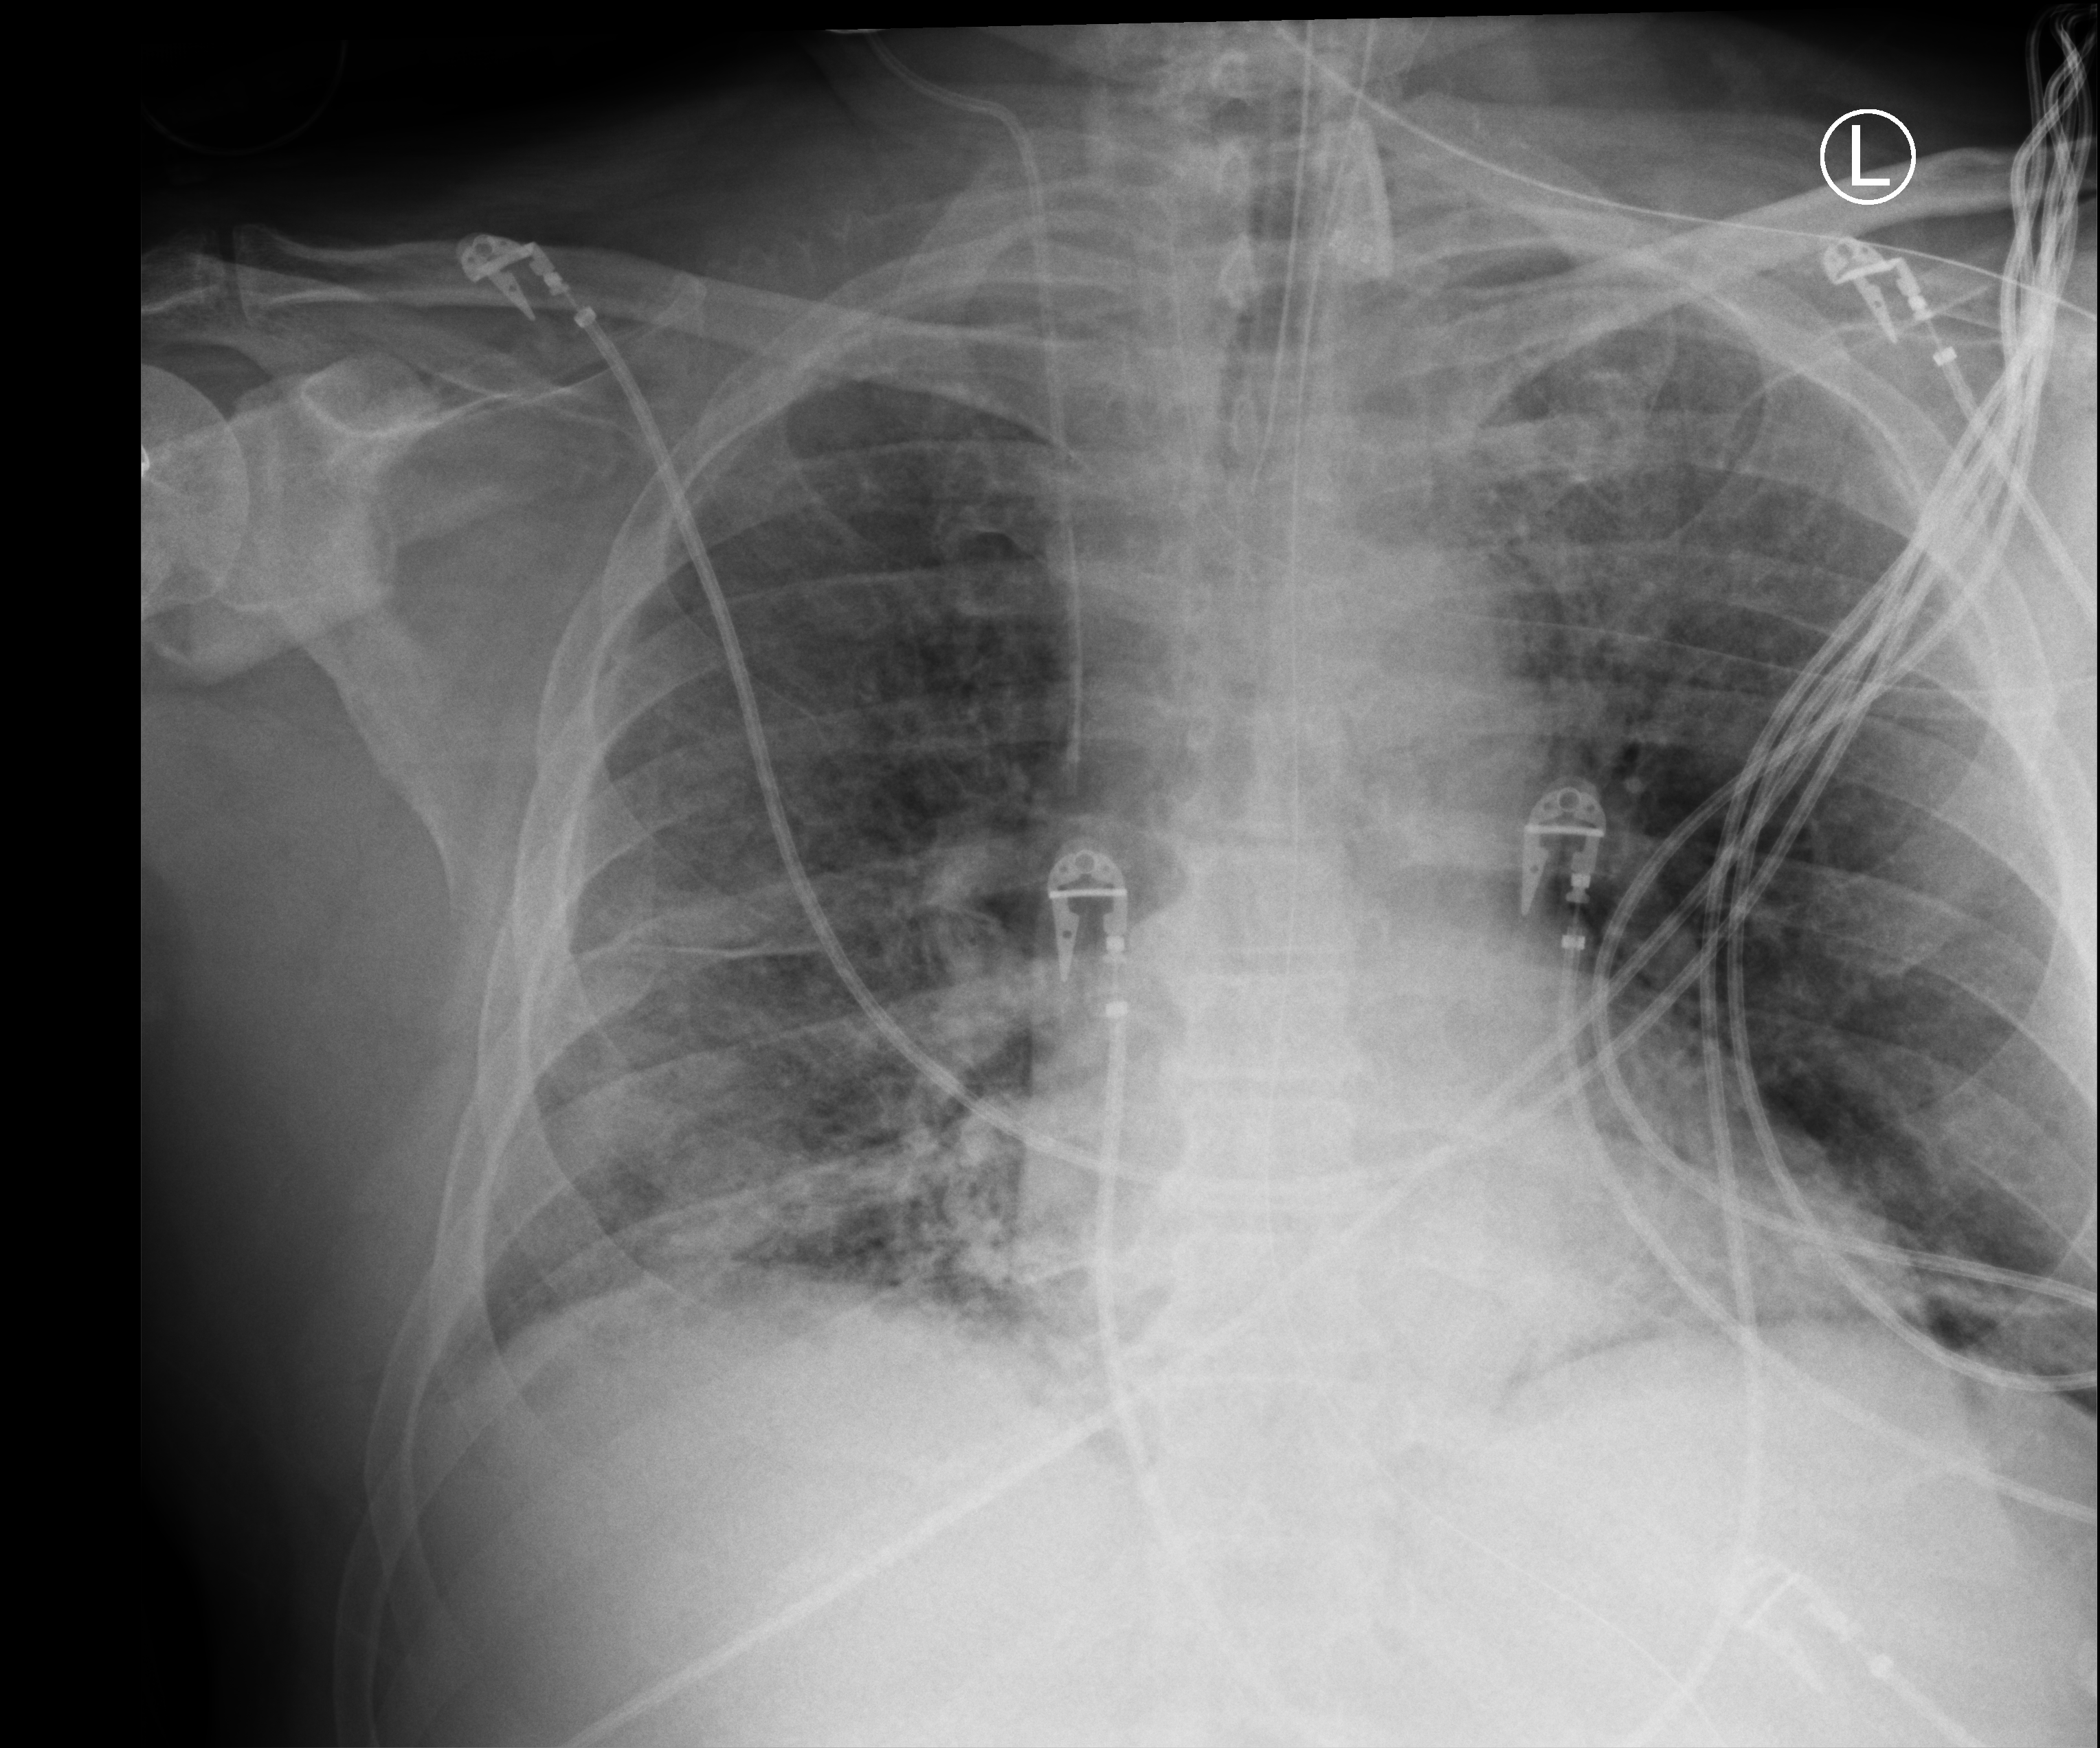
Bedside chest radiograph (computed radiography), anteroposterior (AP) projection. Male patient hospitalised with COVID-19, age 60–74 years.
Hospital-stay facts (about this admission, not read from this image; timing relative to this image not recorded): mechanically ventilated during this hospital stay: yes; other chronic lung disease (admission record): no; admitted to intensive care during this hospital stay: yes.